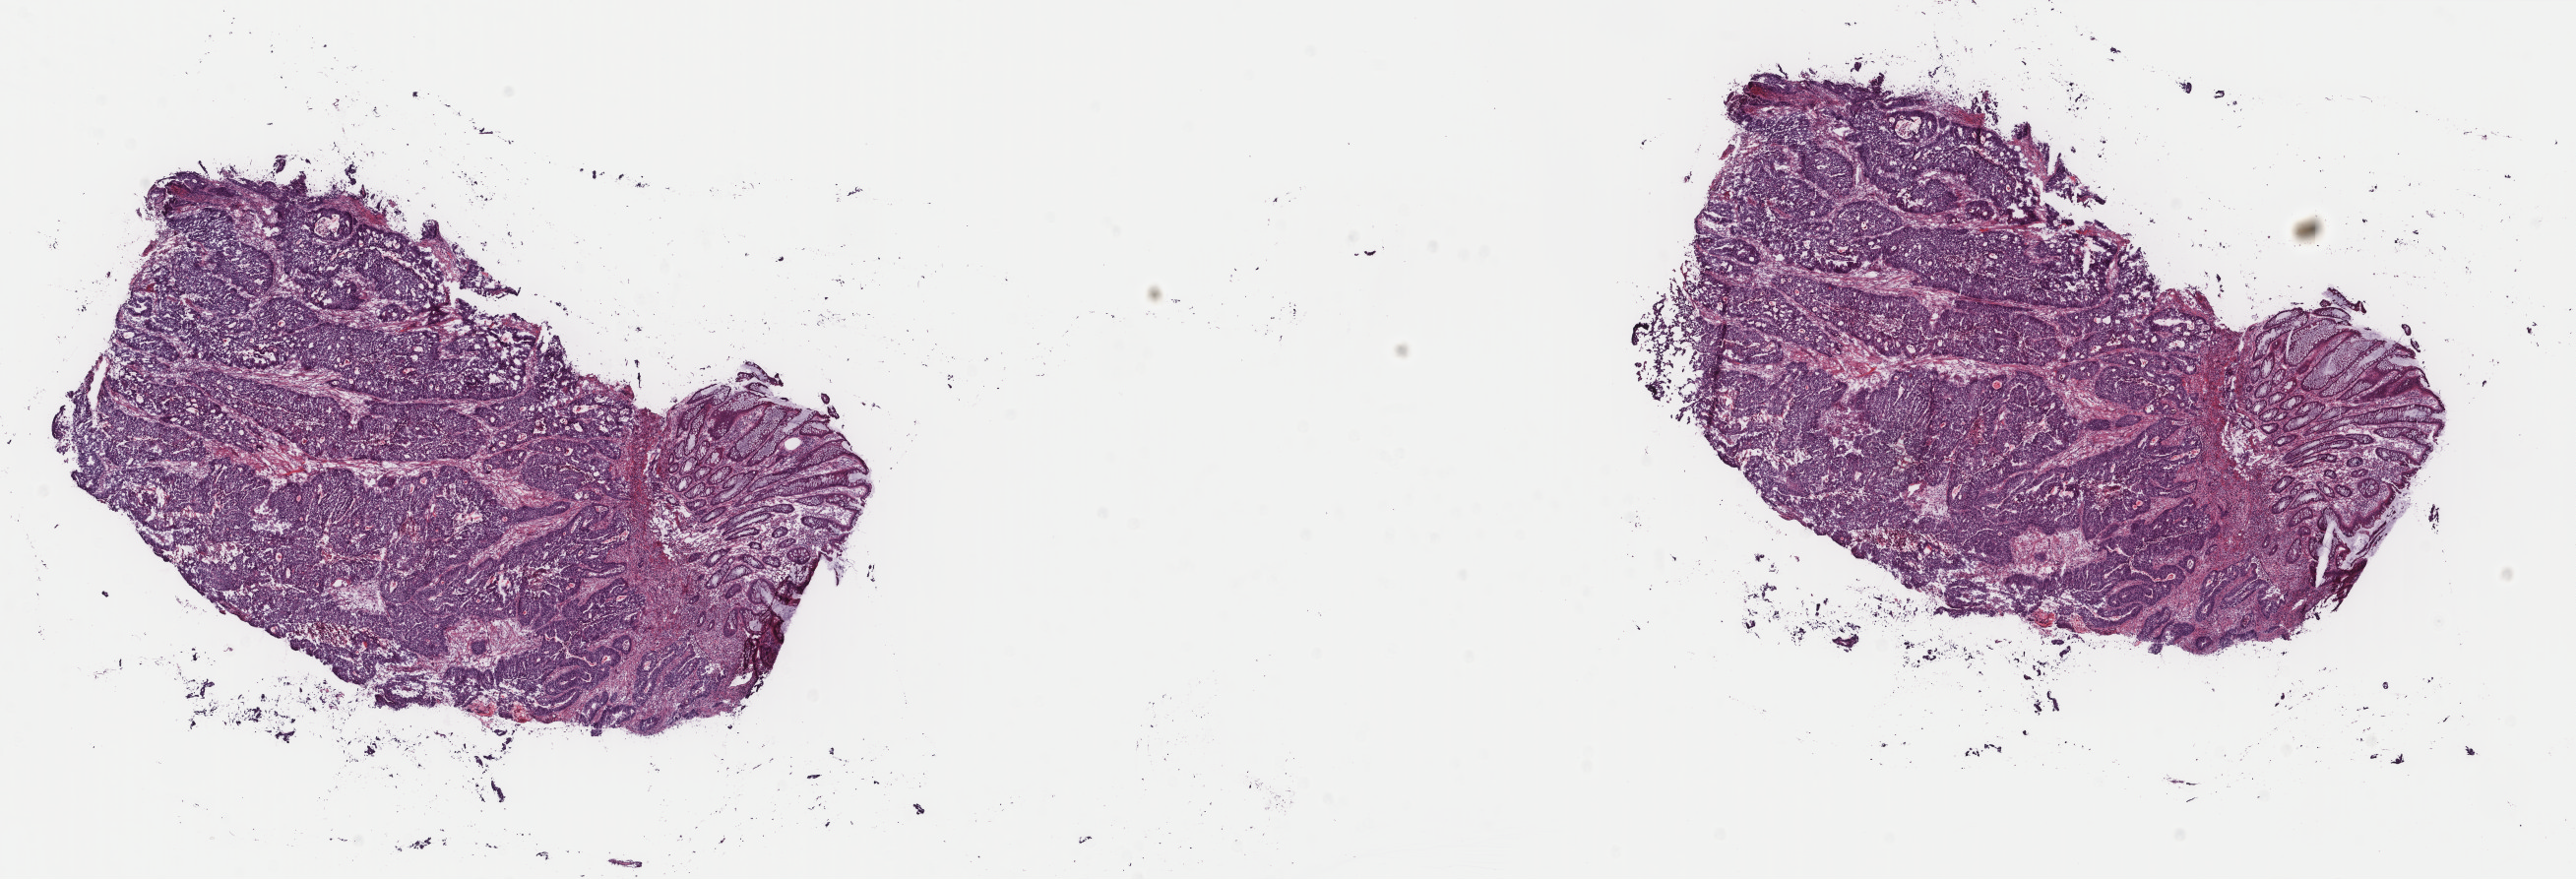
Hematoxylin and eosin (H&E) stained whole-slide image — whole scanned area (about 20.8 x 7.1 mm, from a 40x scan) shown as a low-resolution overview. Frozen section from the top of the tissue portion. Sample: primary tumour, colon. Female, age 68 years at initial diagnosis.
Histologic diagnosis: Adenocarcinoma, NOS.